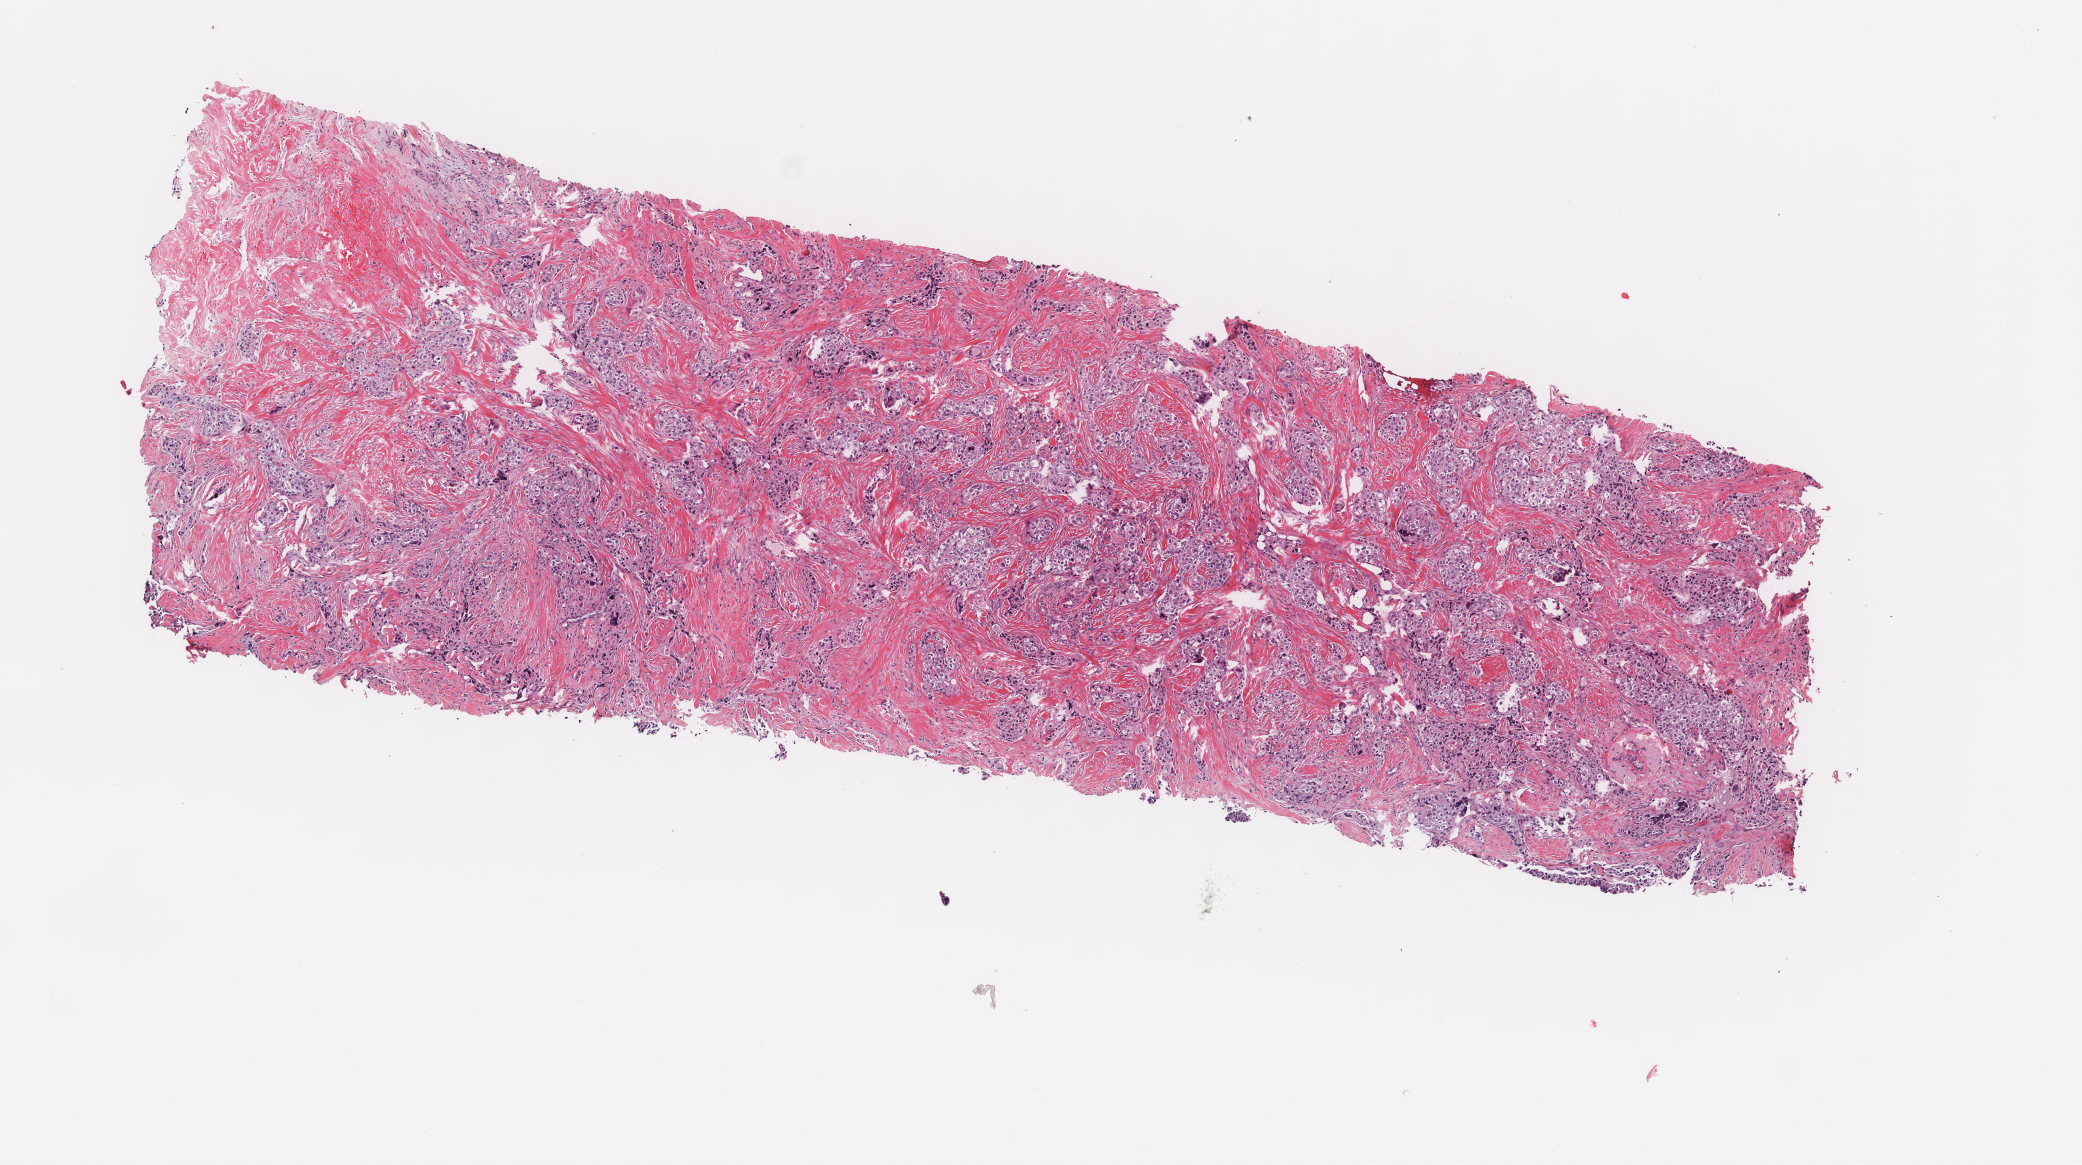
Digitized Hematoxylin and eosin (H&E) stained tissue section (whole slide) — low-resolution overview of the scanned area, about 8.3 x 4.6 mm (slide scanned at 40x). Frozen section. Breast, primary tumour sample. Patient: female, age at initial diagnosis 65 years. Pathologist review of this section (percent, as recorded): tumour cells 50%, tumour nuclei 60%, normal cells 0%, stromal cells 50%, necrosis 0%. Infiltration values recorded for this section: lymphocyte infiltration 0%, monocyte infiltration 0%, neutrophil infiltration 0%.
• histologic diagnosis: Infiltrating duct carcinoma, NOS
• AJCC pathologic stage: IIA (7th edition)